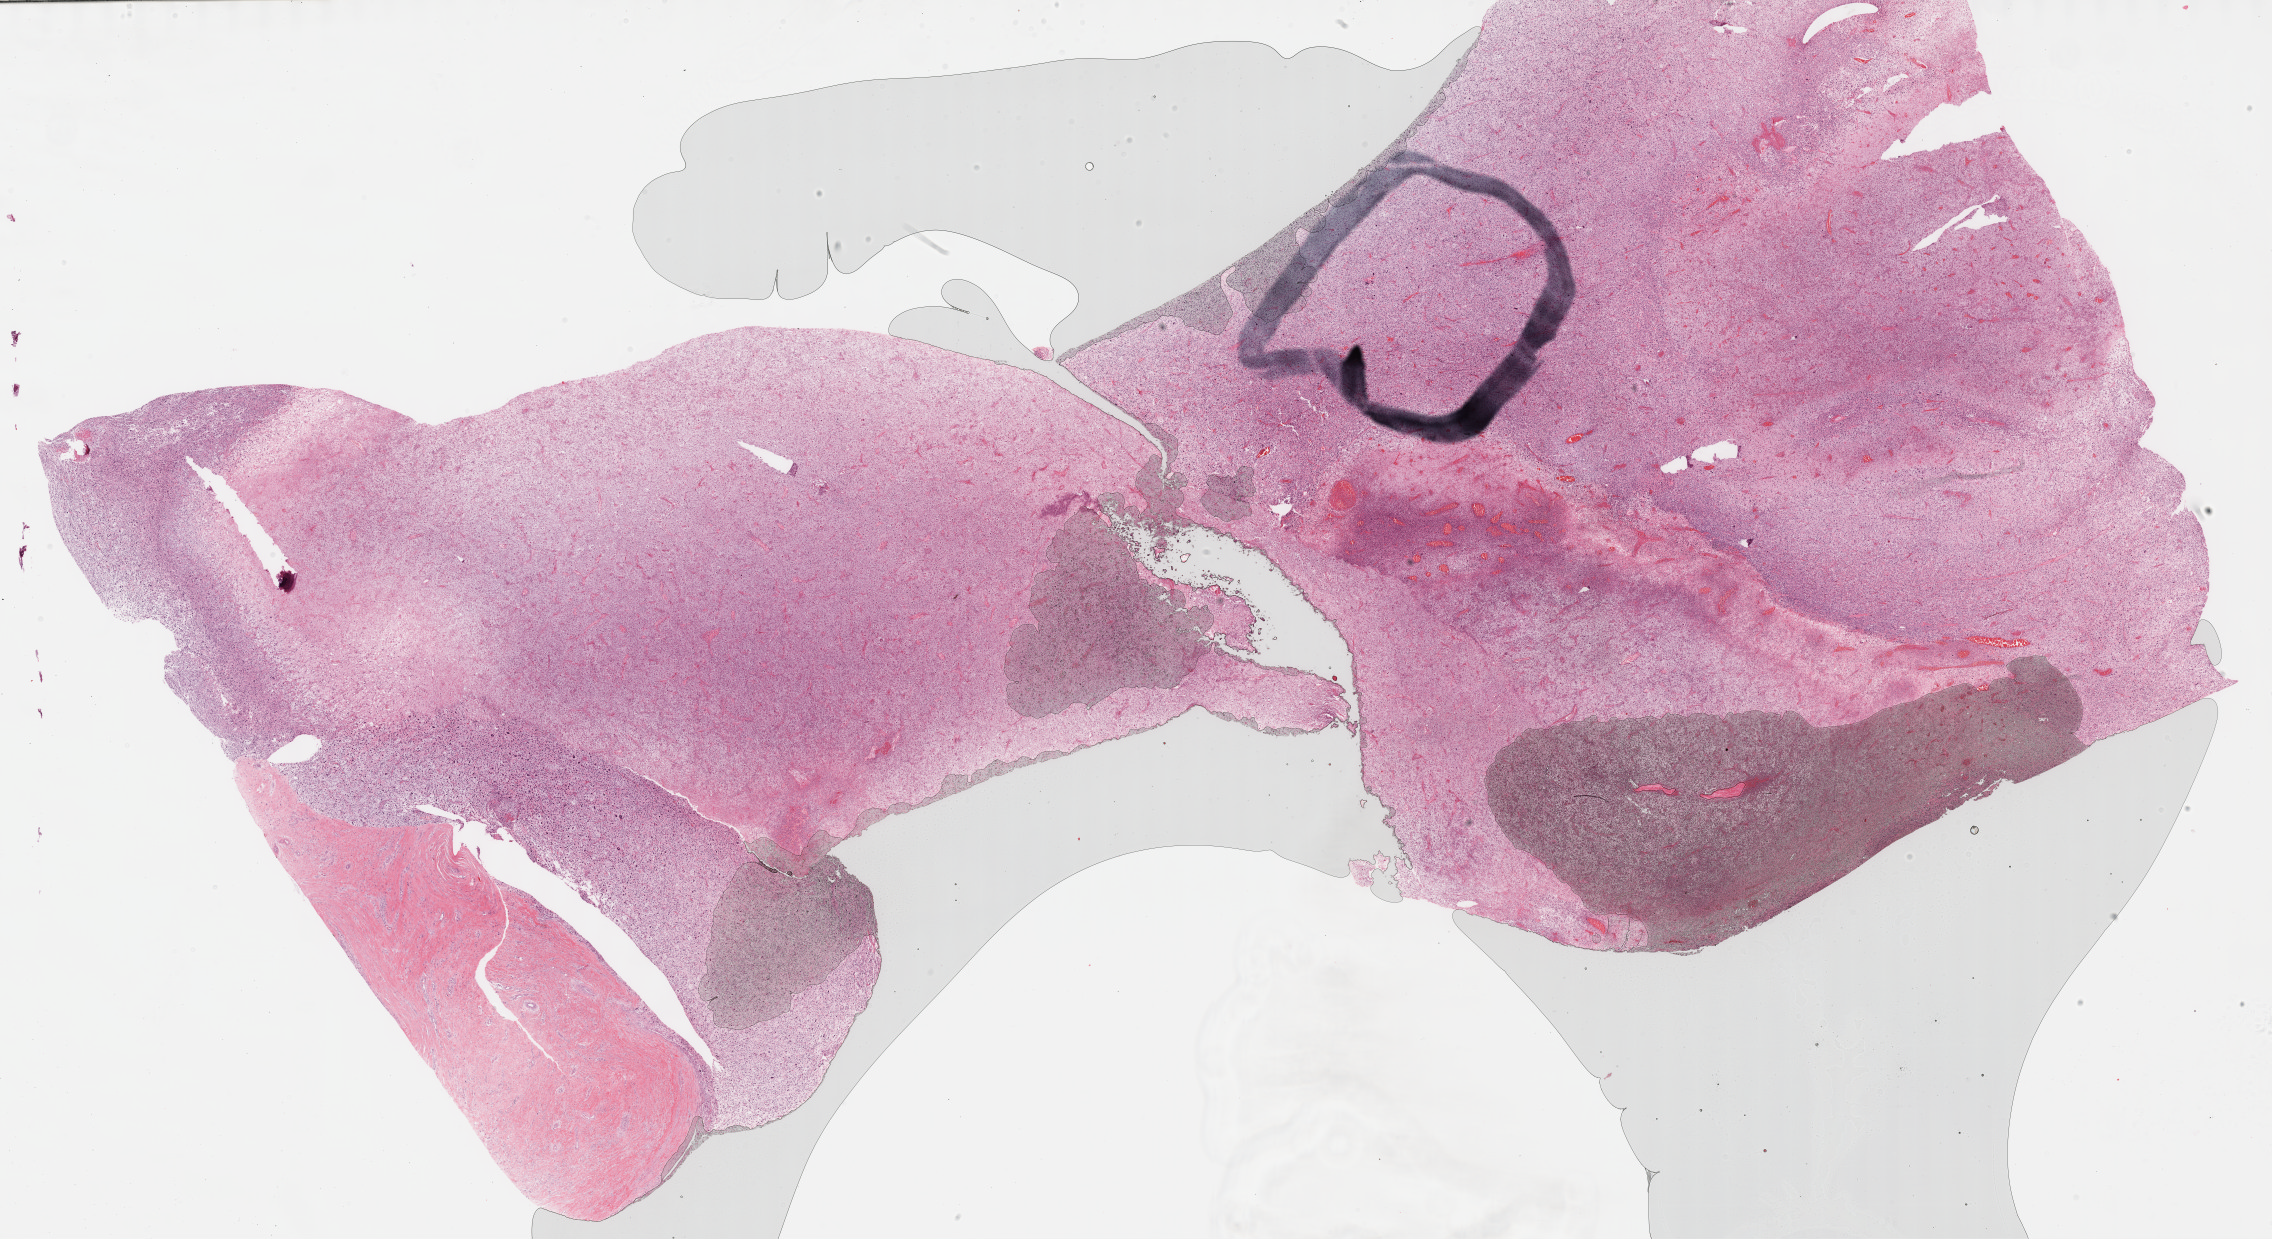
Hematoxylin and eosin (H&E) stained whole-slide image, low-resolution overview of the scanned area, about 36.7 x 20.0 mm (from a 40x scan); formalin-fixed paraffin-embedded (FFPE) diagnostic section; primary tumour sample from the retroperitoneum and peritoneum. Female patient; age at initial diagnosis 55 years.
Diagnosis: Dedifferentiated liposarcoma (retroperitoneum).